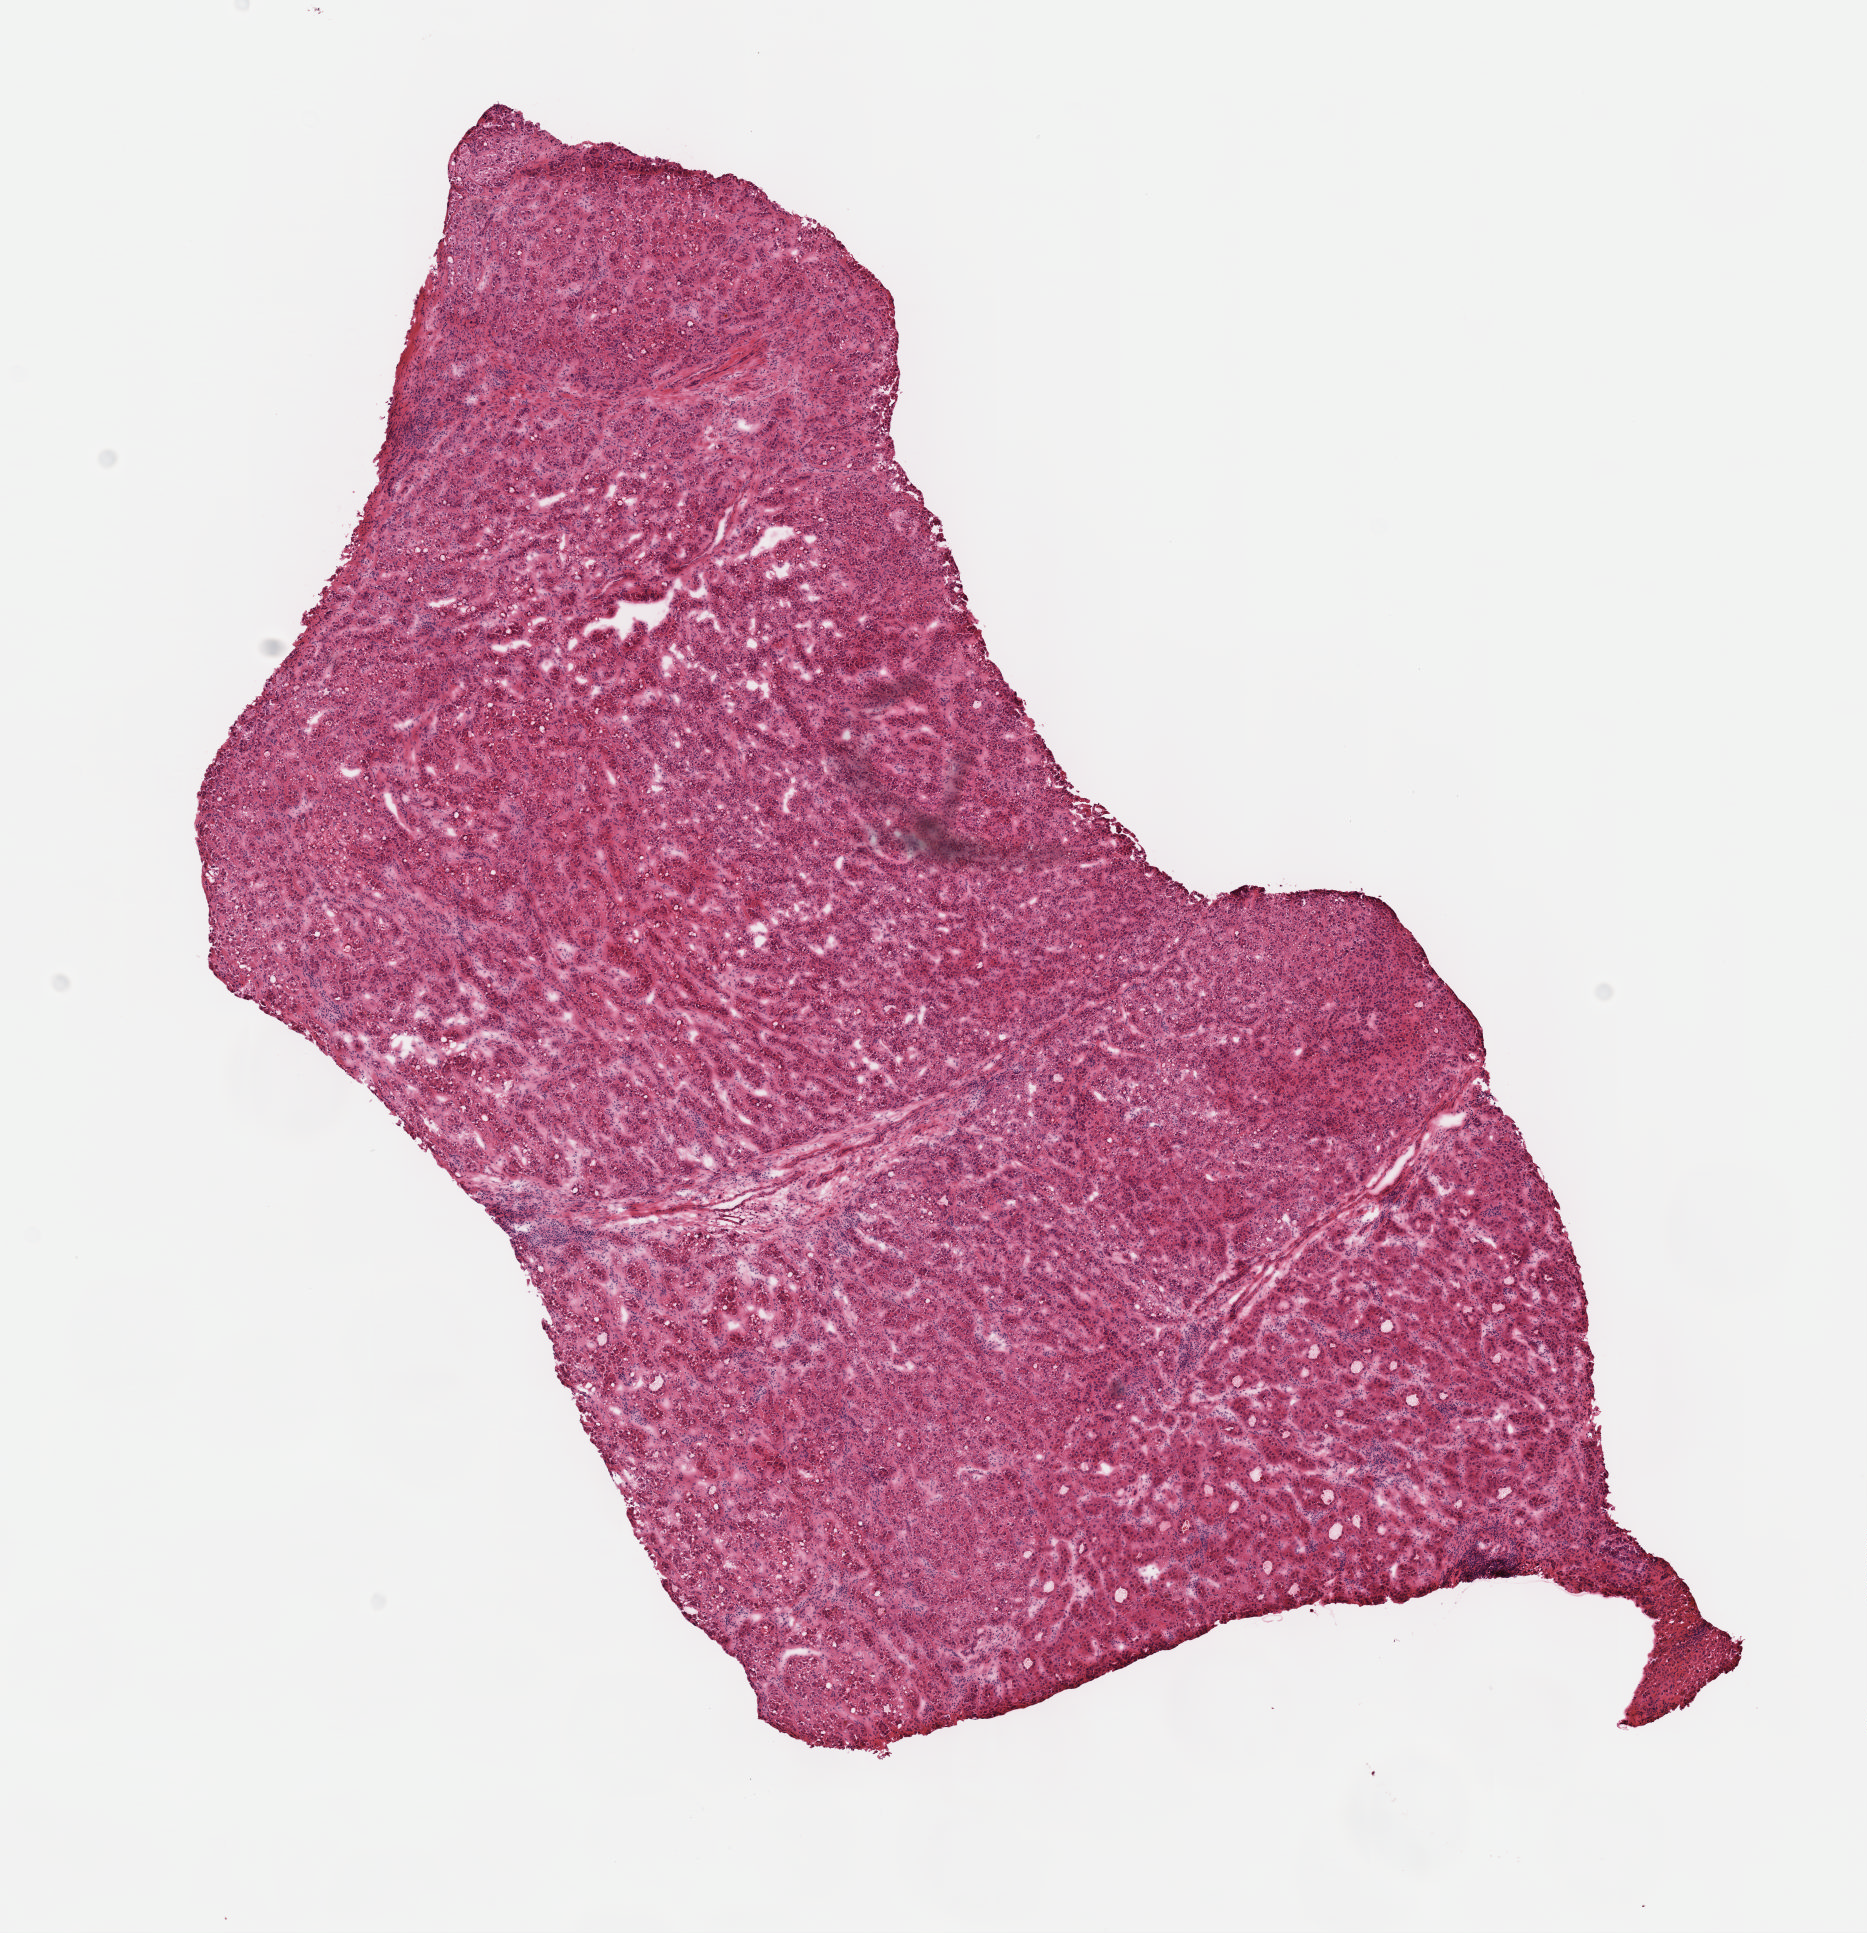
Digitized H&E tissue section (whole slide), low-resolution overview of the scanned area, about 7.6 x 7.8 mm, frozen section from the top of the tissue portion, primary tumour sample from the liver. Patient: male, age at initial diagnosis 43 years. Histologic grade: G2 (moderately differentiated). Slide review estimates, as recorded: tumour cells 90%, tumour nuclei 95%, normal cells 0%, stromal cells 10%, necrosis 0%. Inflammatory infiltration, as recorded: lymphocyte infiltration 0%, monocyte infiltration 0%, neutrophil infiltration 0%.
AJCC pathologic stage: I (7th edition). TNM: T1 N0 M0. Histologic diagnosis: Hepatocellular carcinoma, NOS.